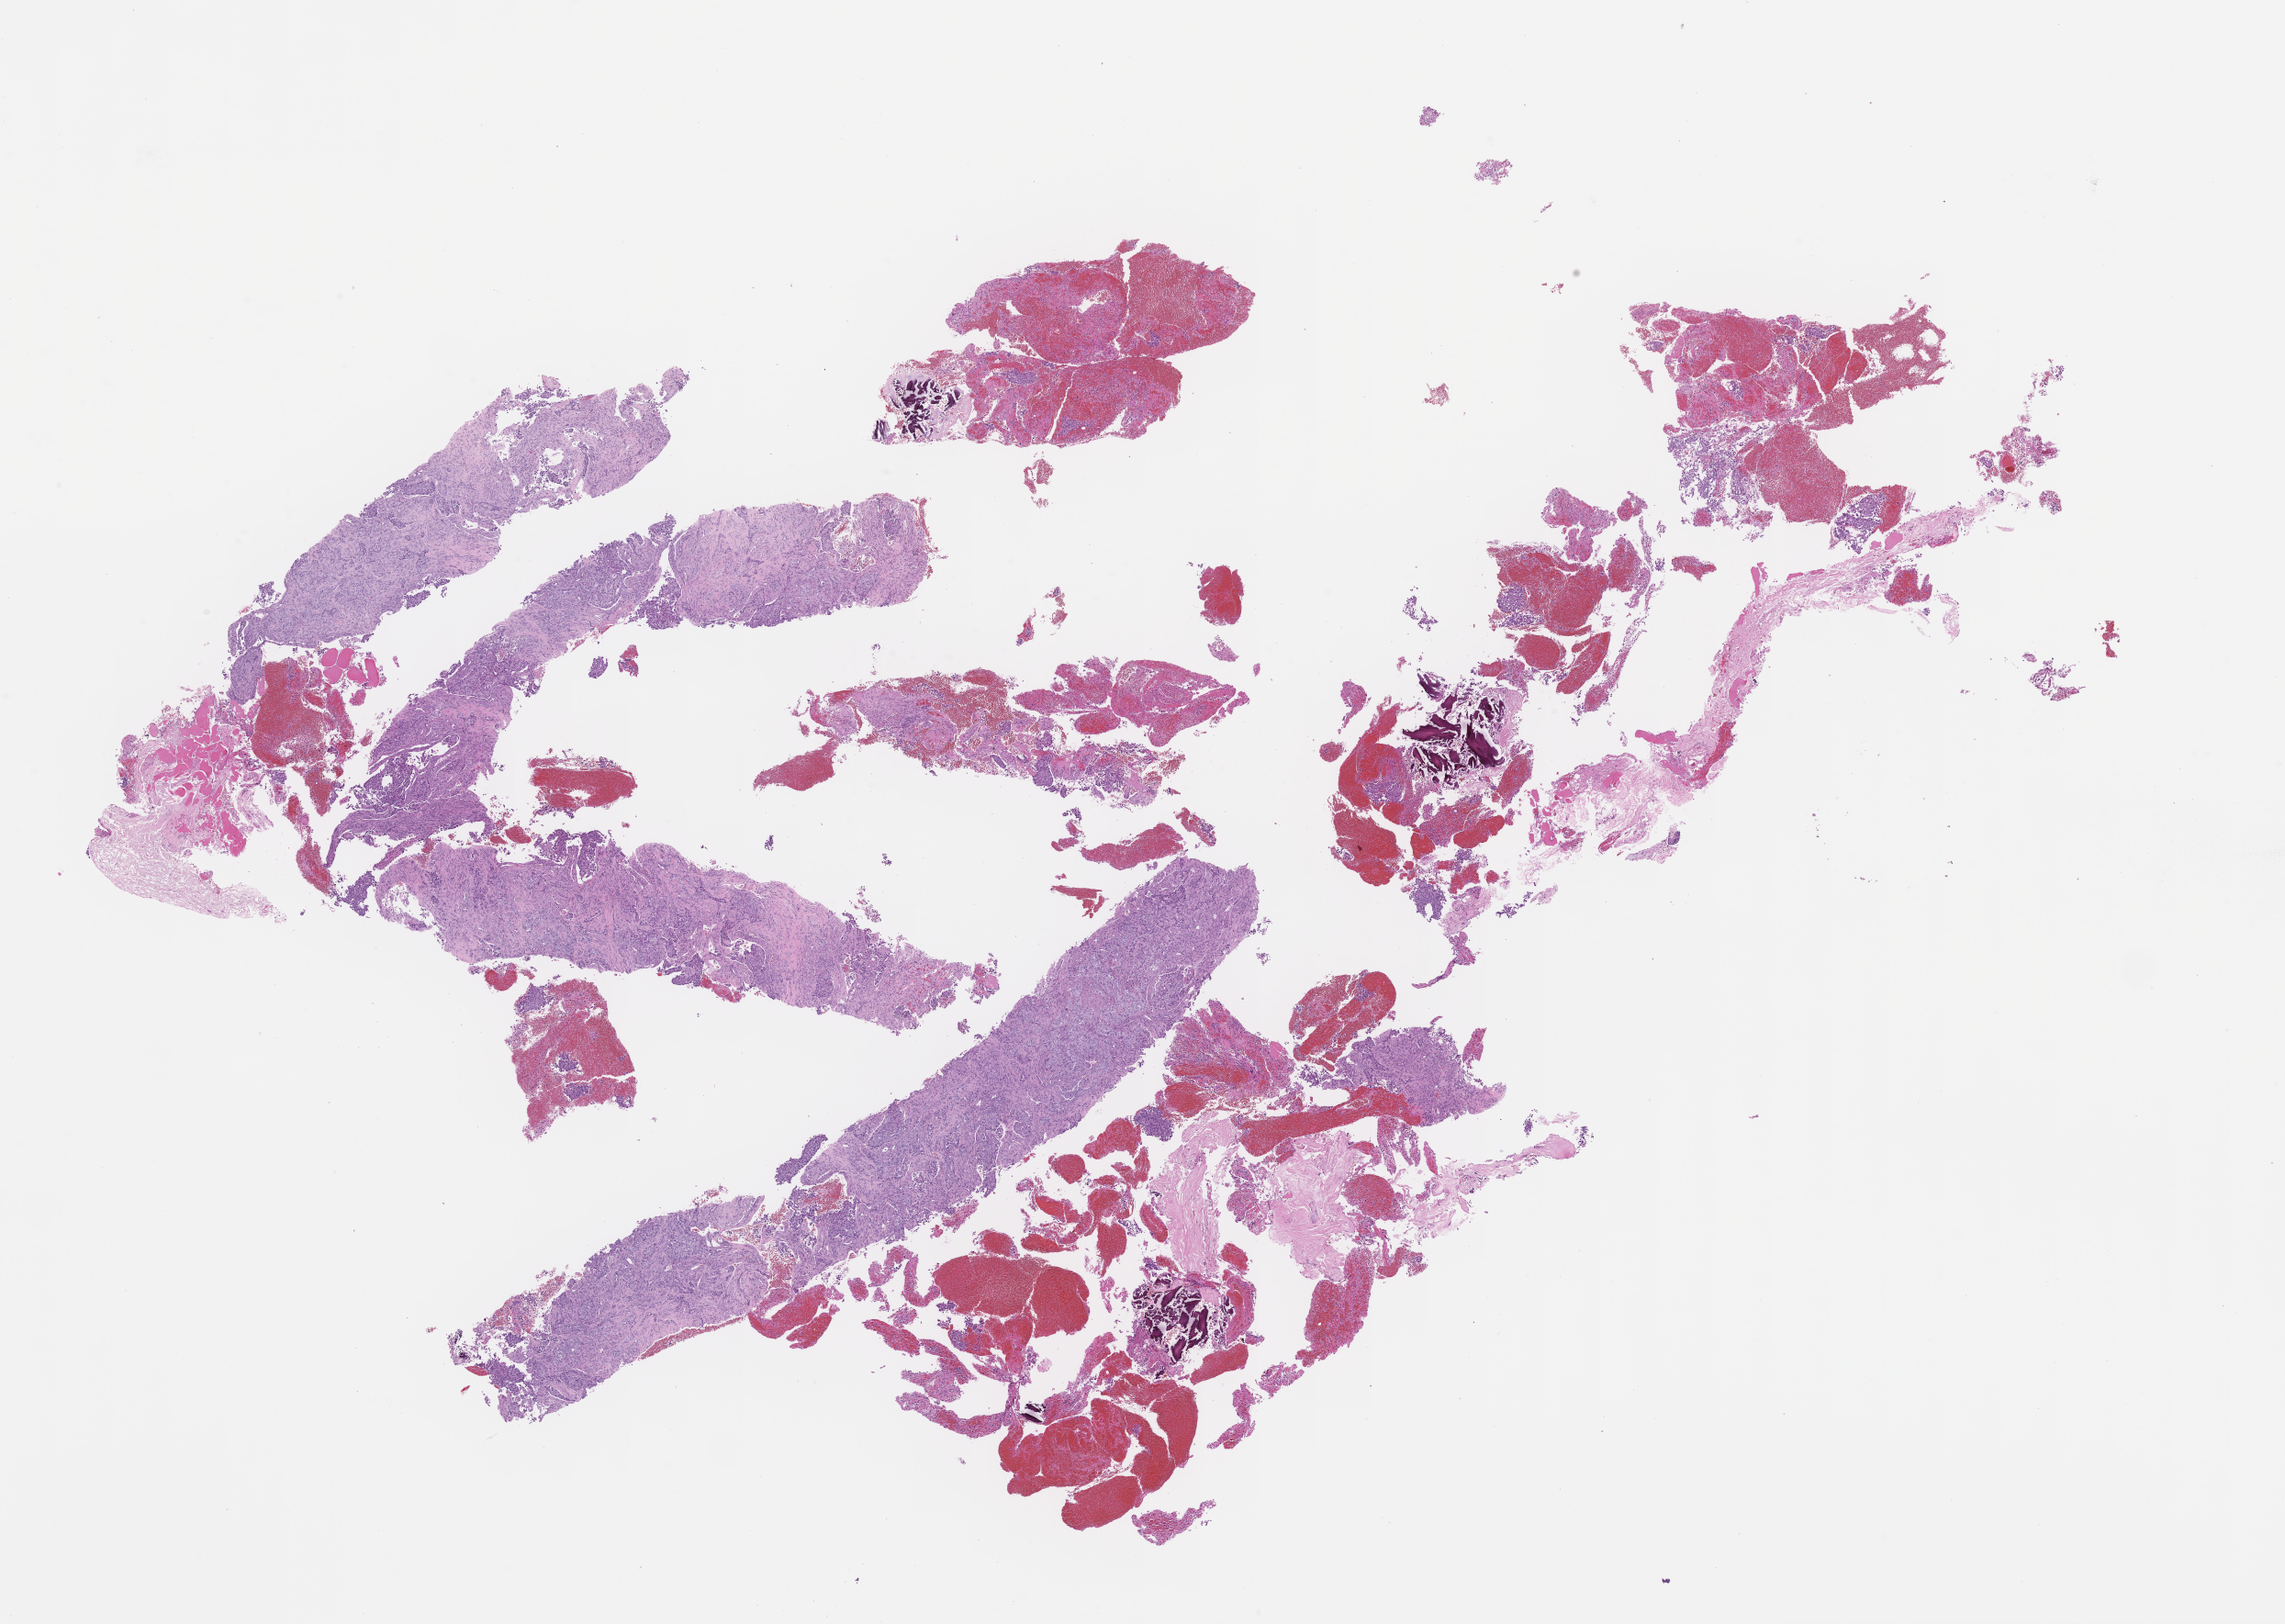
Digitized haematoxylin and eosin-stained section — low-resolution overview of the scanned area, about 20.1 x 14.3 mm. Formalin-fixed paraffin-embedded section. Collected at disease progression. Male patient.
This section: metastatic tumor tissue. Patient diagnosis (primary): Non-Small Cell Lung Carcinoma.